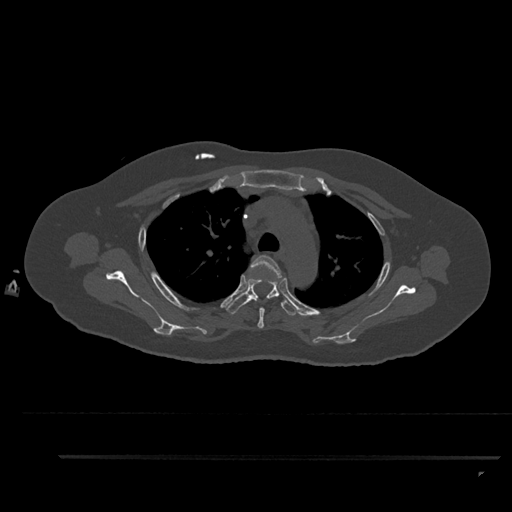
CT including the spine, one axial slice; position 660 of 797 along the scan axis; 120 kVp; bone window (W 1800 / L 400 HU); 0.5 mm slice thickness; 512 × 512 image matrix, field of view 408 × 408 mm. Female patient, age 44 years. From the clinical record (not read from this slice): primary cancer: renal.
Outlined on this slice (semi-automatic segmentation, software-assisted and operator-edited):
- T3 vertebra: box from (x=250, y=255) to (x=282, y=328) px
- T4 vertebra: (x=226, y=278)–(x=299, y=315)